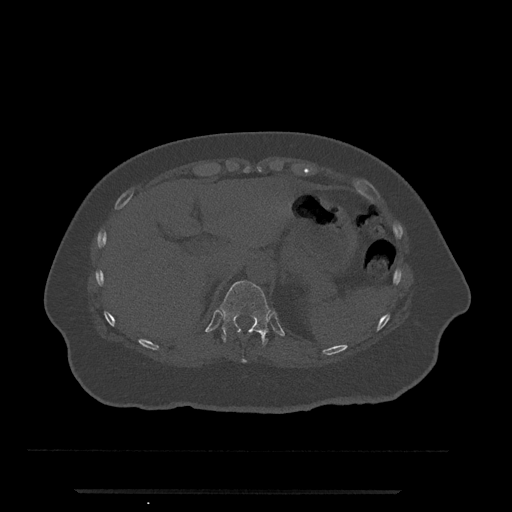
CT including the spine, one axial slice. Reconstruction kernel Br40s/3. 120 kVp. Bone window (W 1800 / L 400 HU). 512 × 512 image matrix, field of view 440 × 440 mm. Female patient, age 51 years. Case-level facts recorded for this patient, not image findings: primary cancer: neuro; vertebrae with lytic lesions (as recorded): T8.
Structures marked on this image (semi-automatically segmented with operator editing):
- T10 vertebra: bounding box <241,358,247,363> (left, top, right, bottom; pixels)
- T11 vertebra: <220,281,271,346>